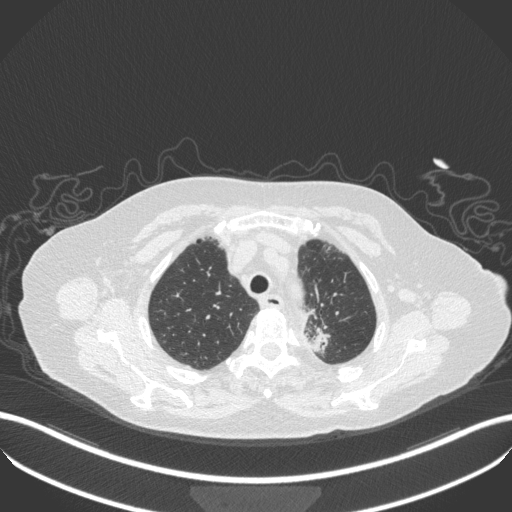
Chest CT, one axial slice. Slice 277 of 353 in the series (ordered by position). Lung window (W 1500 / L -600 HU). 1 mm slice thickness. 512 × 512 image matrix, field of view 400 × 400 mm. Female patient, age 81 years. From the clinical record (not read from this slice): clinical TNM (as recorded): T2a N0 M0.
Structures marked on this image (rectangle marked by the reading radiologist):
- lung tumour (recorded histology: adenocarcinoma): bounding box [x1, y1, x2, y2] px = [278, 306, 339, 356]